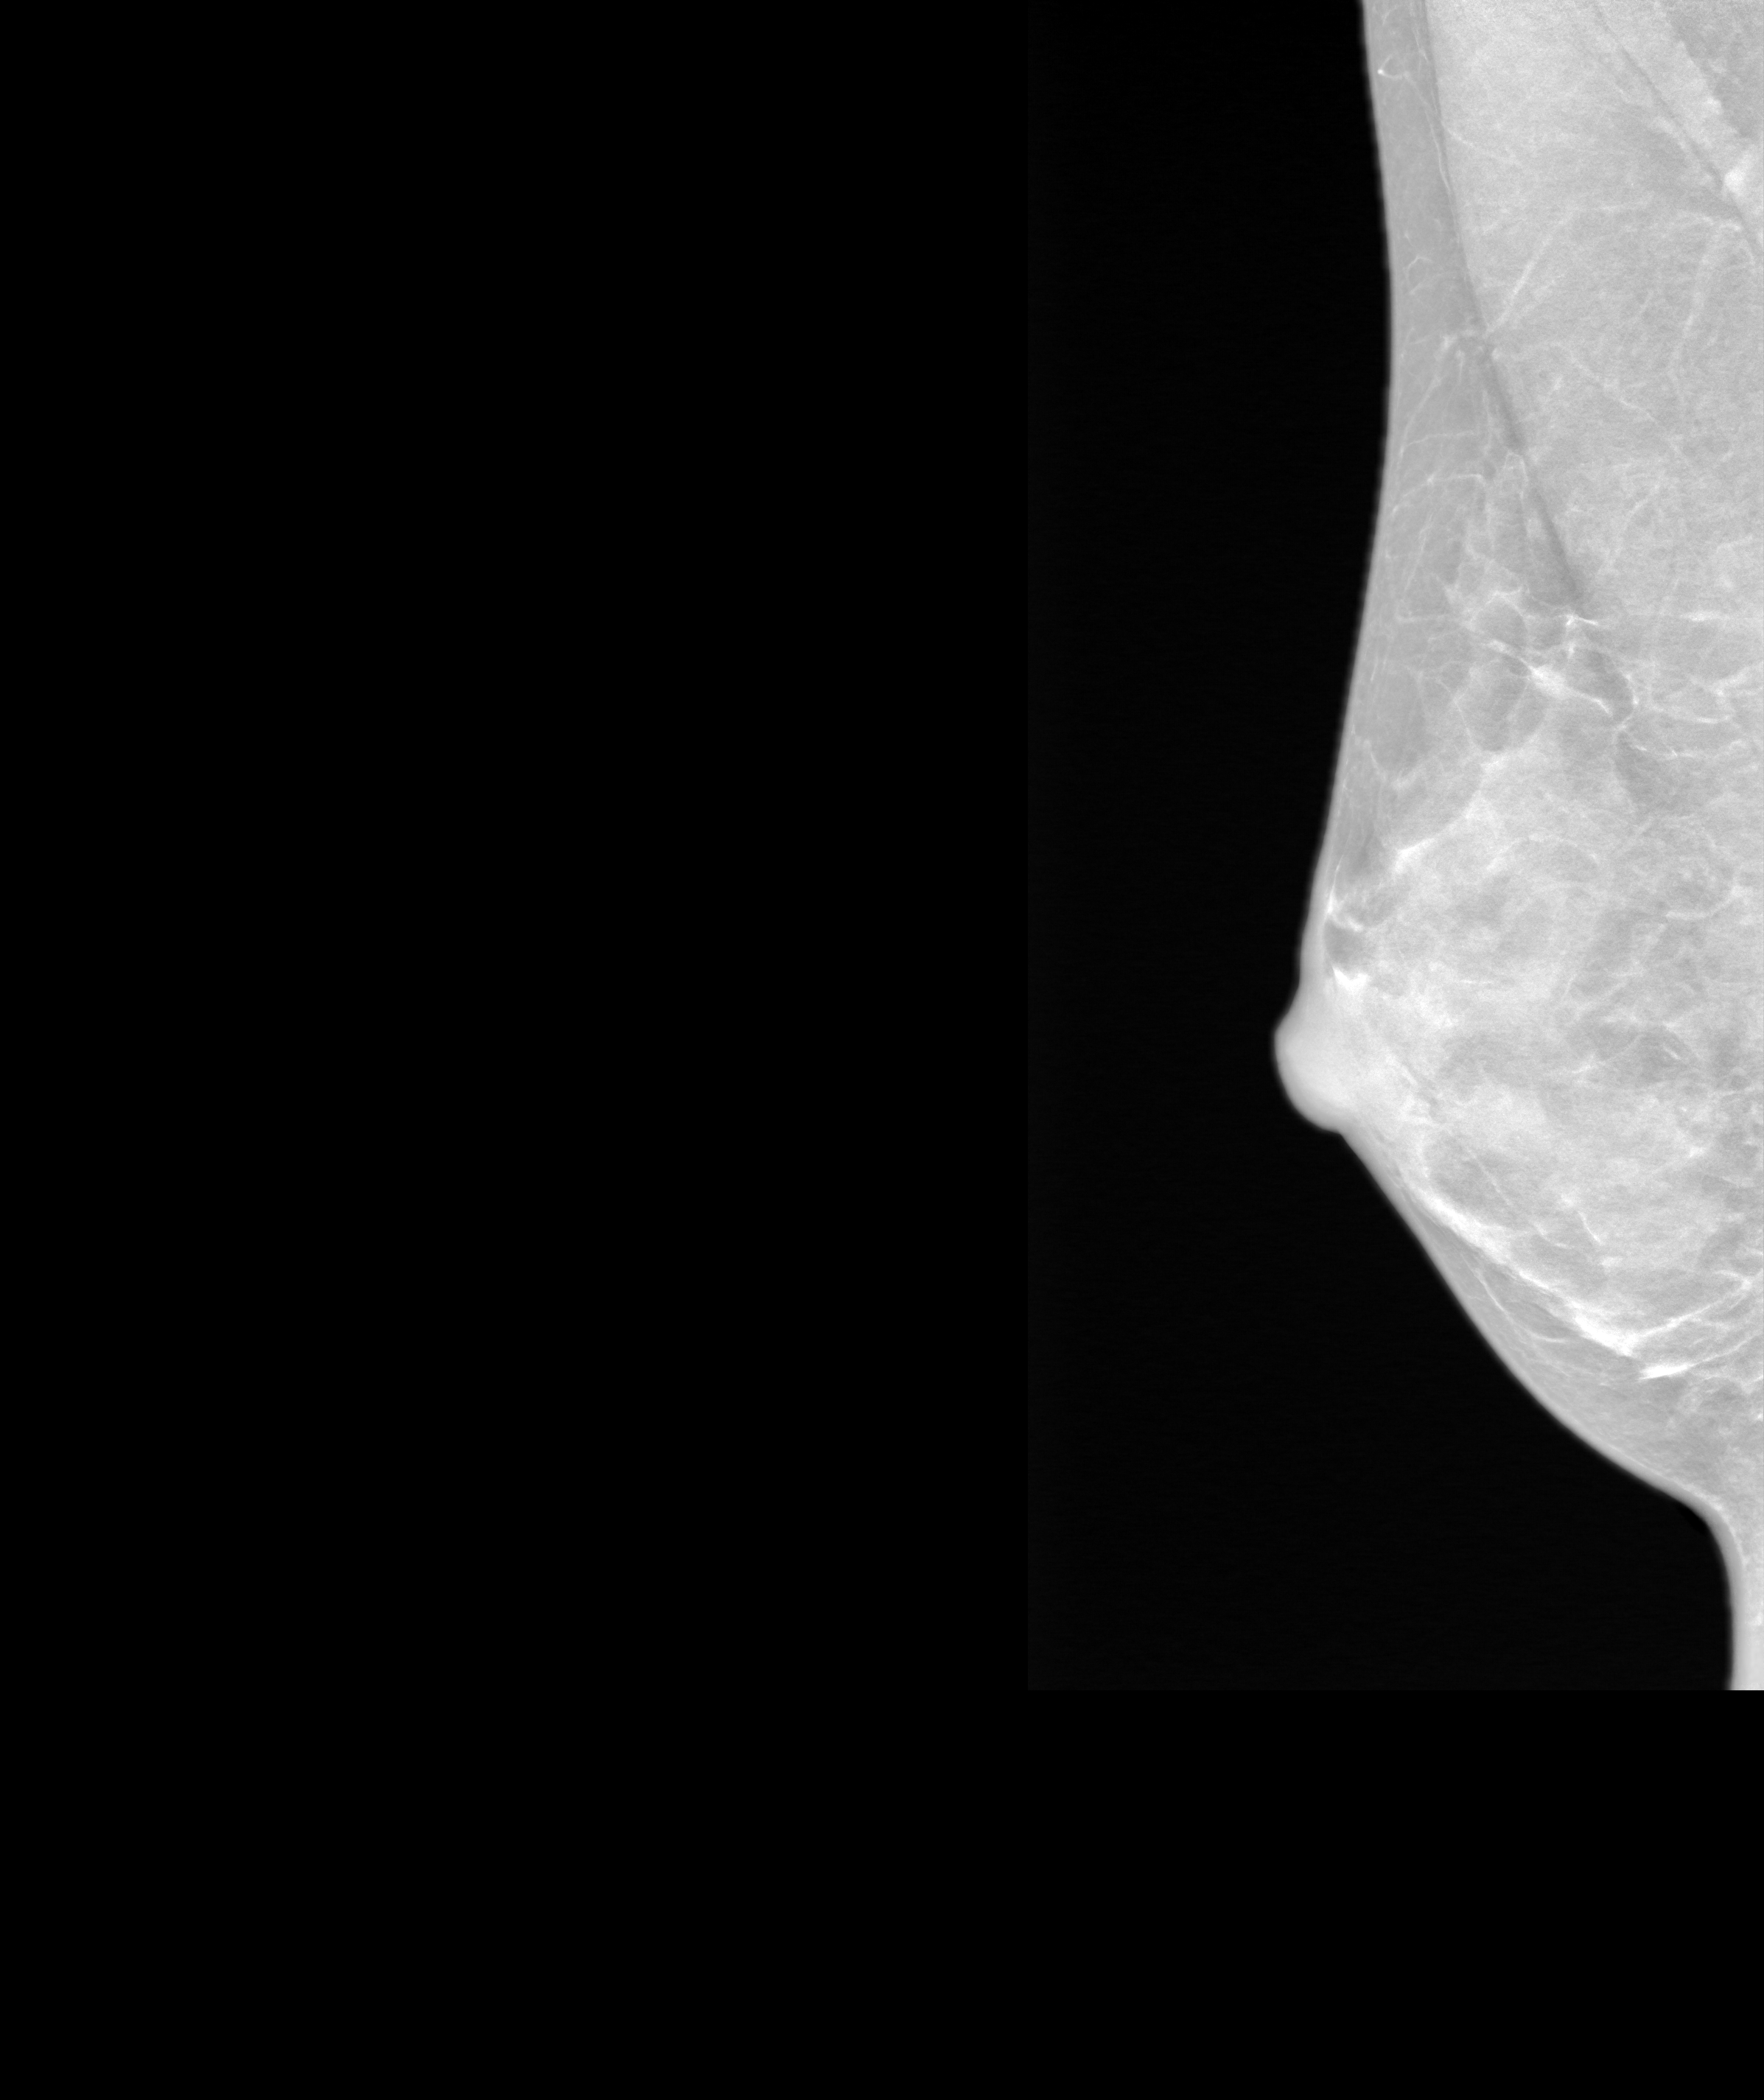
Annual screening mammography examination, system: SenoIris_1SP2(440). Patient aged 47 years (female).
Image type: synthesized 2-D view from tomosynthesis. Breast: right. Projection: MLO view.